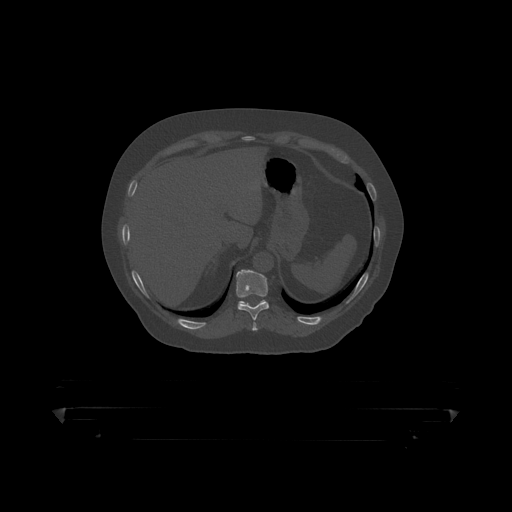
CT including the spine, one axial slice. Reconstruction kernel STANDARD. 120 kVp. Bone window (W 1800 / L 400 HU). 1.25 mm slice thickness. 512 × 512 image matrix, field of view 650 × 650 mm. Patient: male, 60 years. Case-level facts recorded for this patient, not image findings: primary cancer: prostate.
Structures marked on this image (semi-automatically segmented with operator editing):
- T10 vertebra: bounding box <236,270,269,319> (left, top, right, bottom; pixels)
- T11 vertebra: <239,300,265,305>